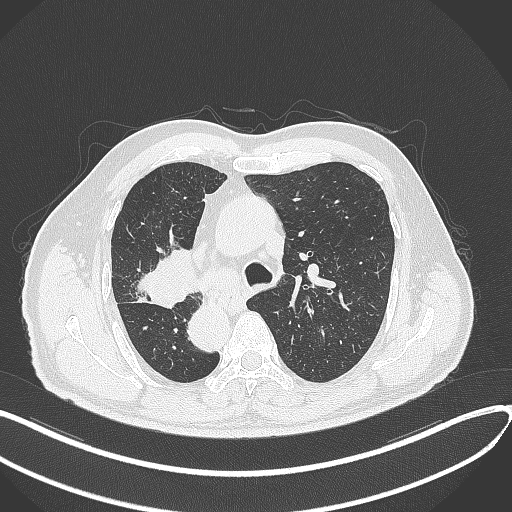
Chest CT, one axial slice; slice 208 of 300 in the series (ordered by position); lung window (W 1500 / L -600 HU); 1 mm slice thickness; 512 × 512 image matrix, field of view 400 × 400 mm. Male patient, age 67 years. From the clinical record (not read from this slice): clinical TNM (as recorded): T2a N0 M0.
Outlined on this slice (rectangle marked by the reading radiologist):
- lung tumour (recorded histology: squamous cell carcinoma): box from (x=132, y=237) to (x=207, y=313) px